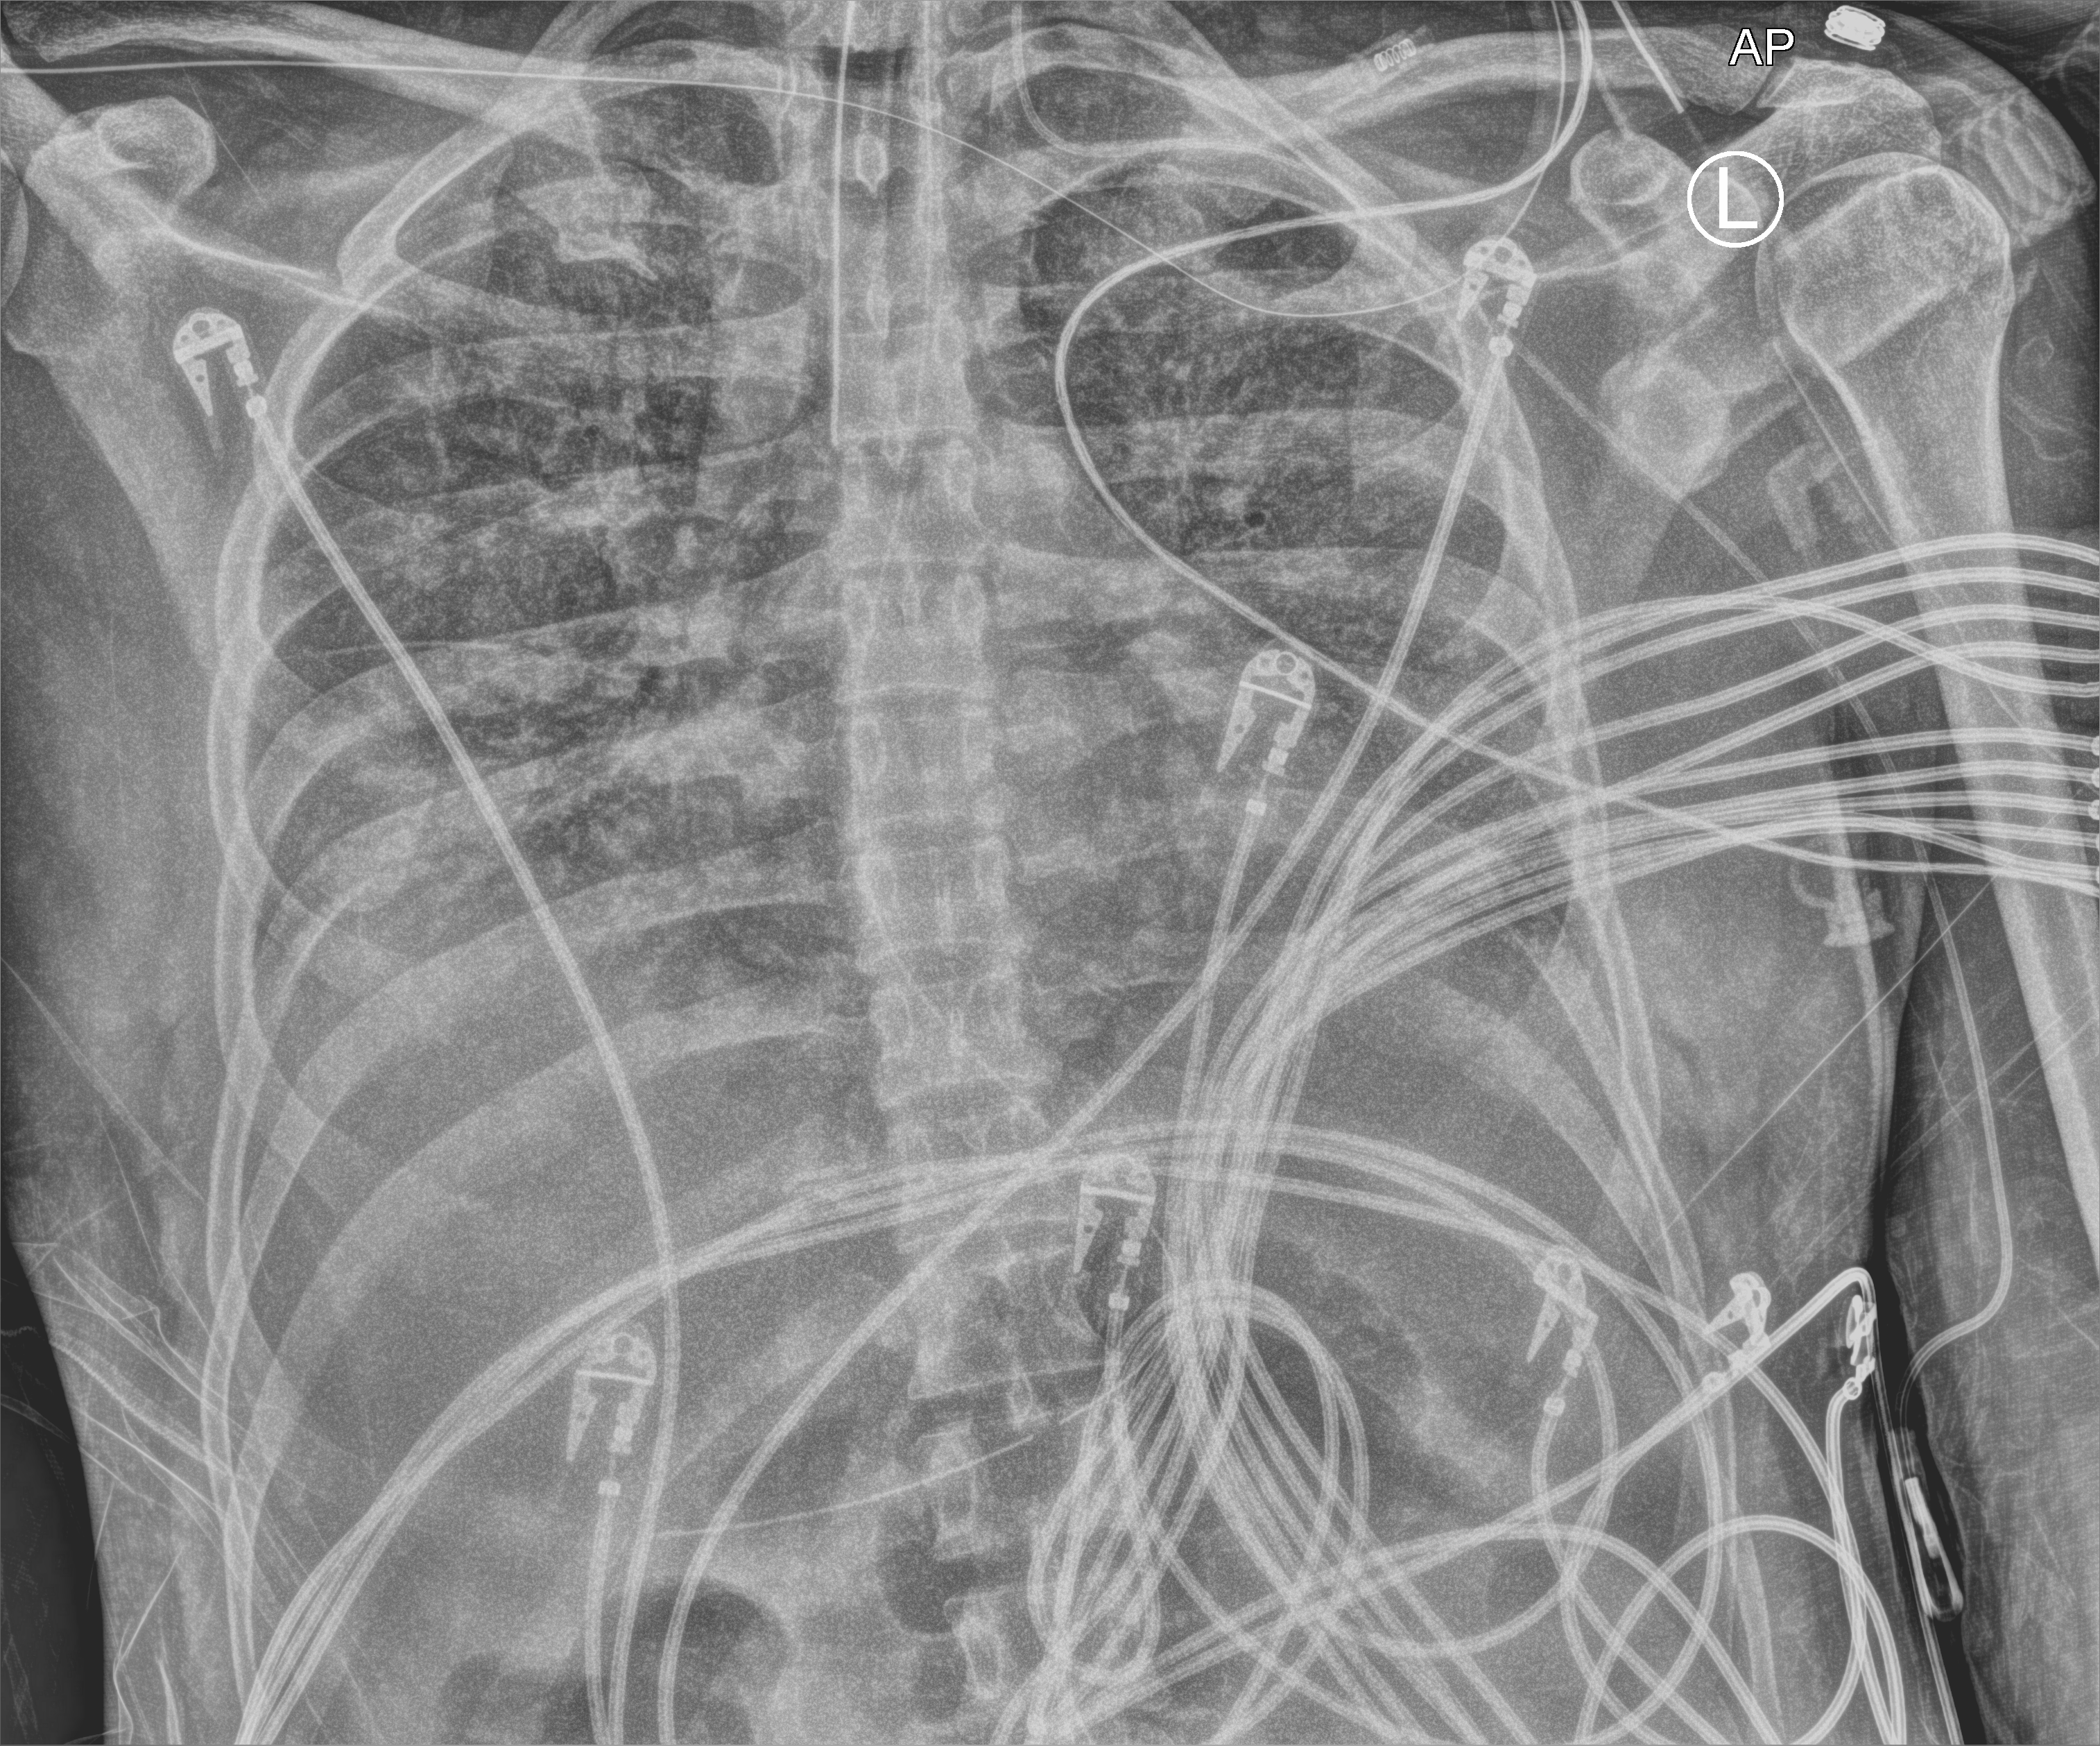
Portable chest radiograph; anteroposterior (AP) projection. Male patient hospitalised with COVID-19, age 18–59 years.
Admission-level facts for this patient (not findings on this image; timing relative to this image not recorded): hypertension (admission record): no; mechanically ventilated during this hospital stay: yes.